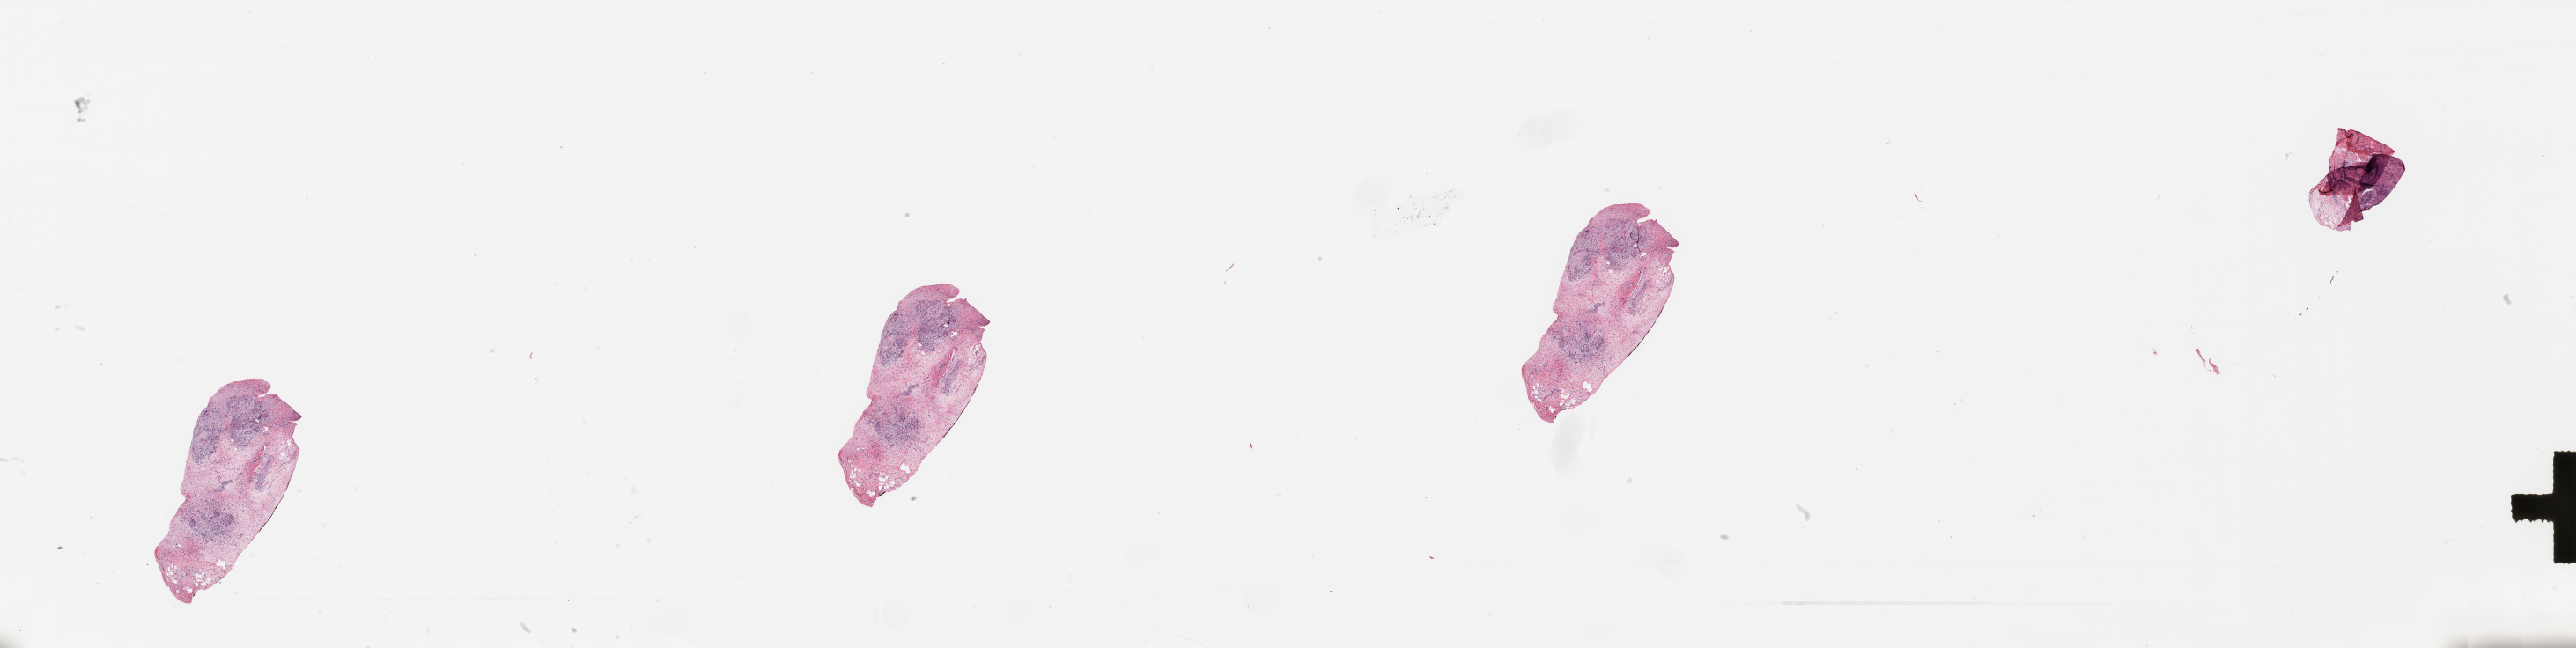
Hematoxylin and eosin (H&E) stained whole-slide image, low-resolution overview of the scanned area, about 46.3 x 11.6 mm (acquisition: 20x scan). Tumour tissue sample, pancreas. 65-year-old male patient. Histologic grade: G3 (poorly differentiated).
- diagnosis: Infiltrating duct carcinoma, NOS
- AJCC pathologic stage: IIB
- primary tumour site (as recorded): head